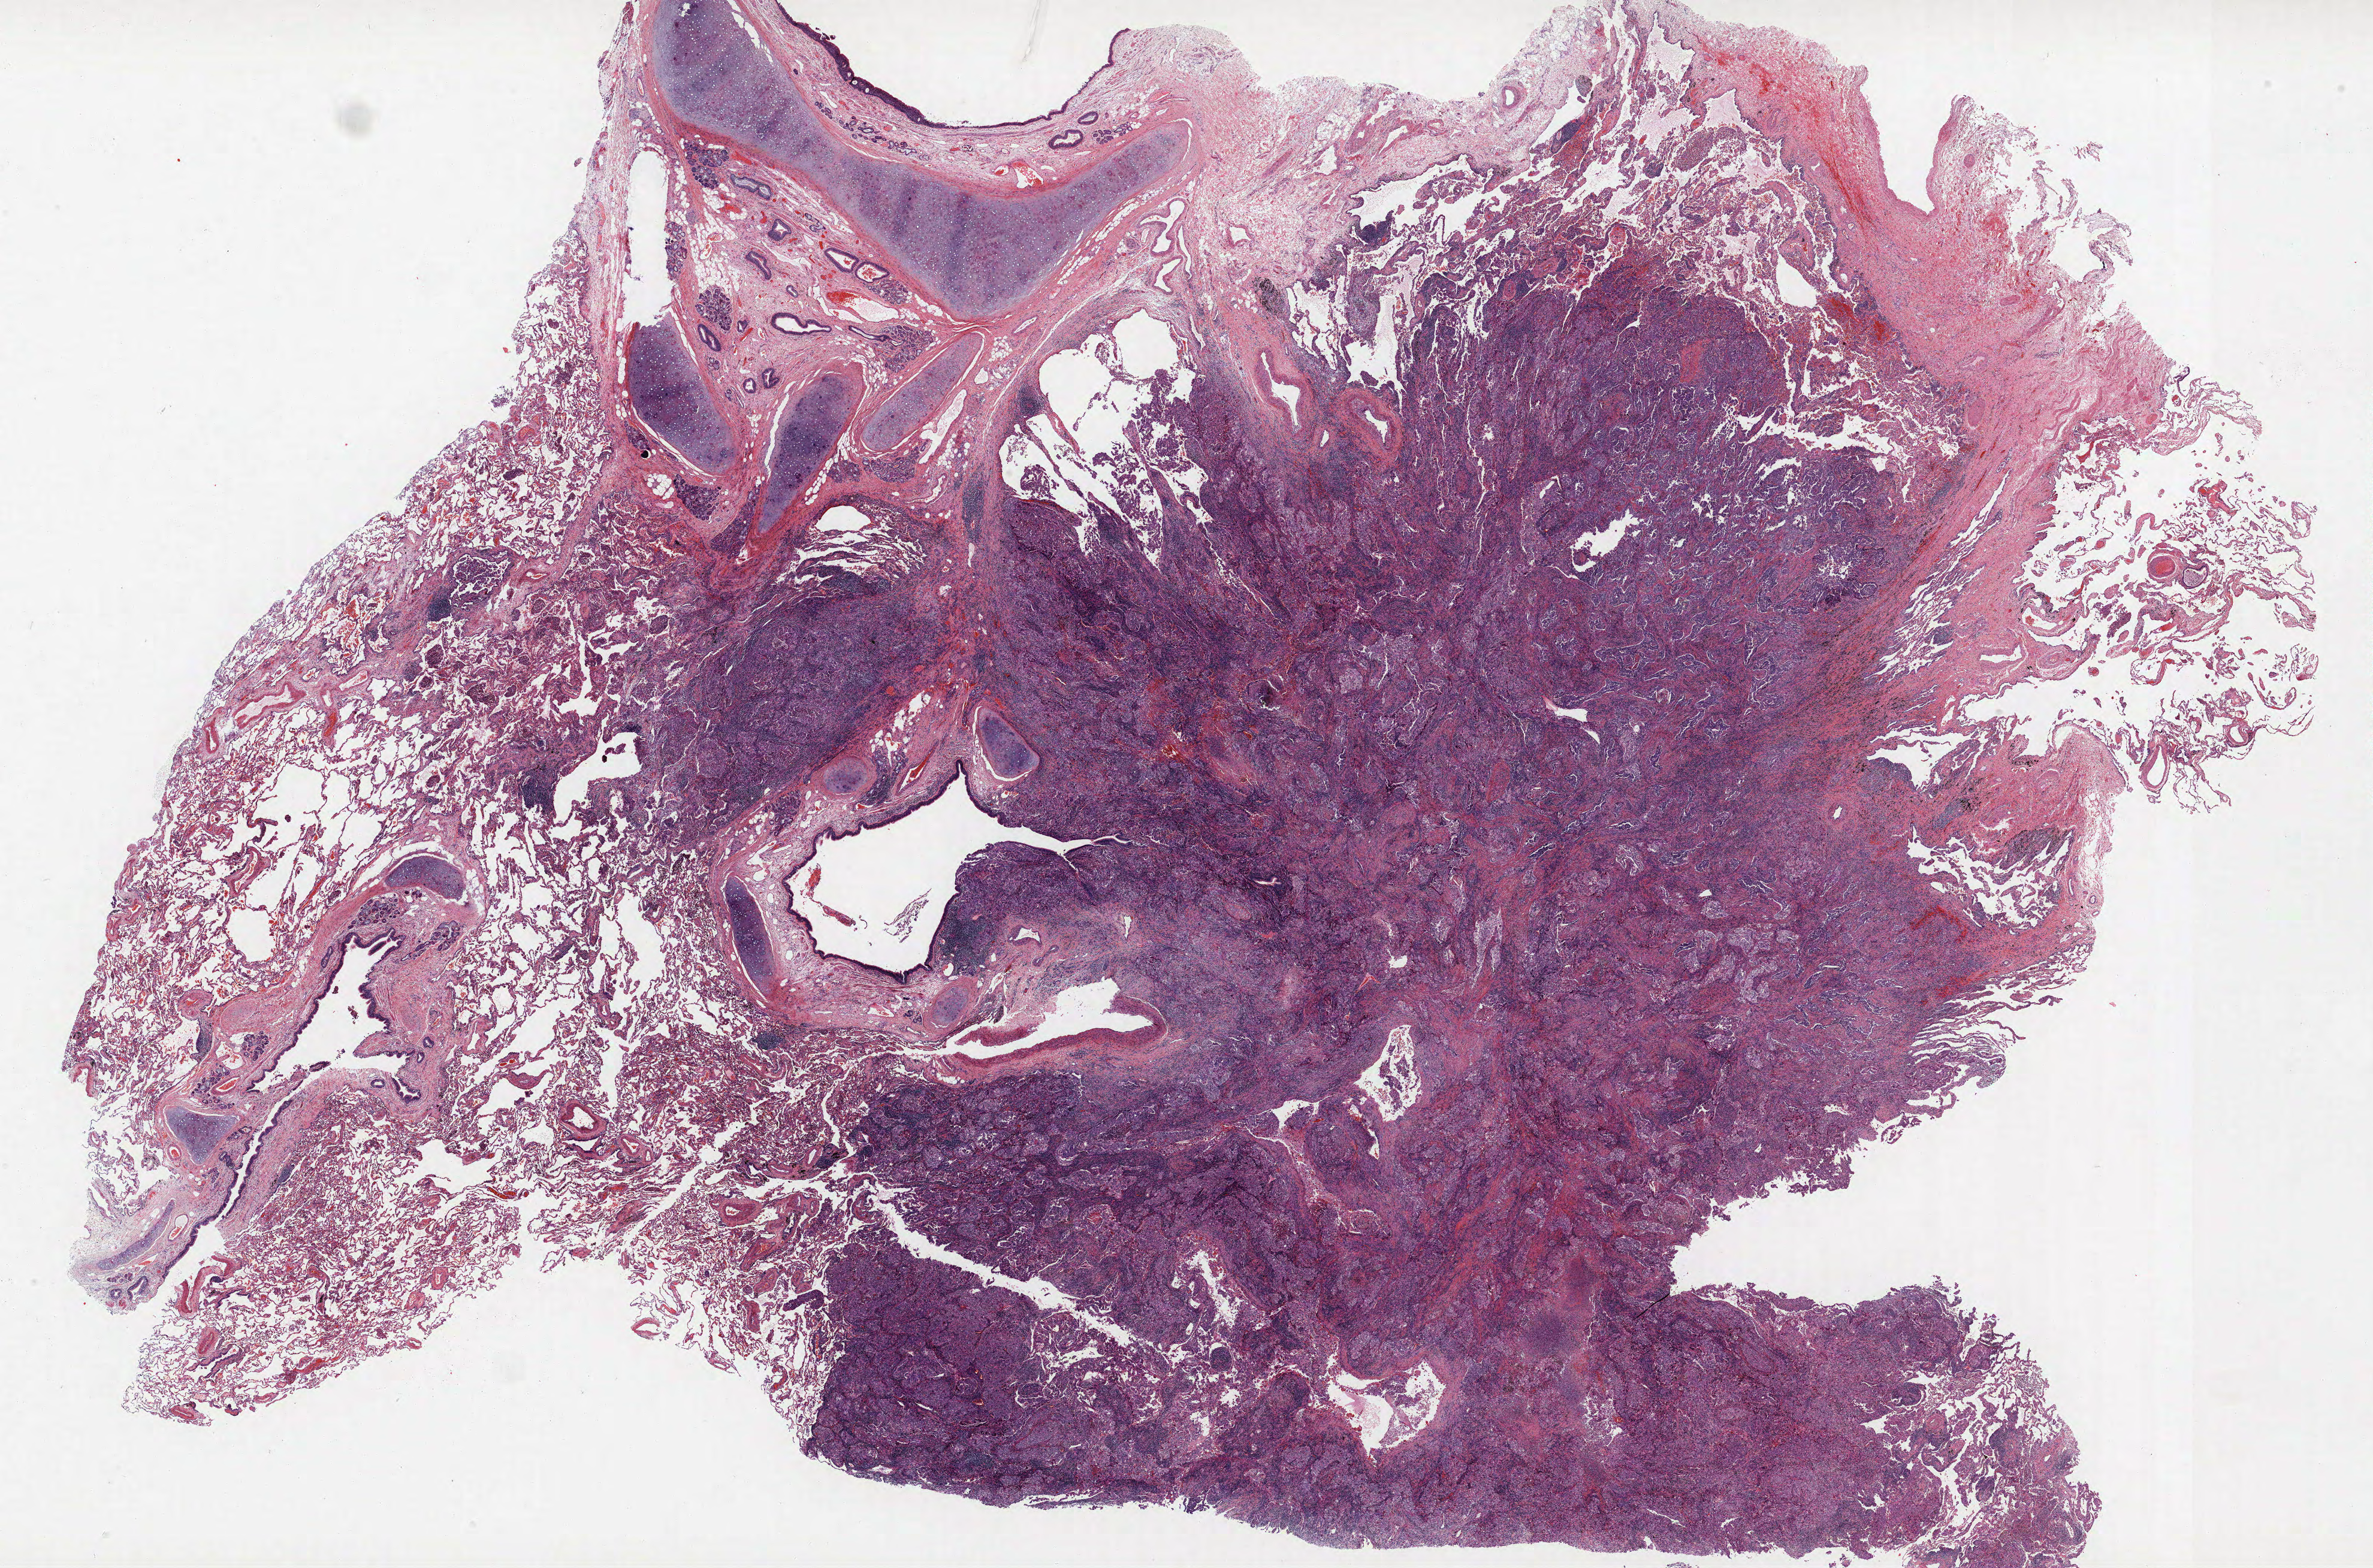
Whole-slide histology image, H&E — a low-resolution overview of the entire scanned area, about 31.7 x 20.9 mm (acquisition: 40x scan). Formalin-fixed paraffin-embedded (FFPE) section. Lung. Male, age 59 at enrolment. Current smoker at enrolment.
Participant's lung-cancer diagnosis: Large cell carcinoma, NOS (ICD-O-3 8012/3).